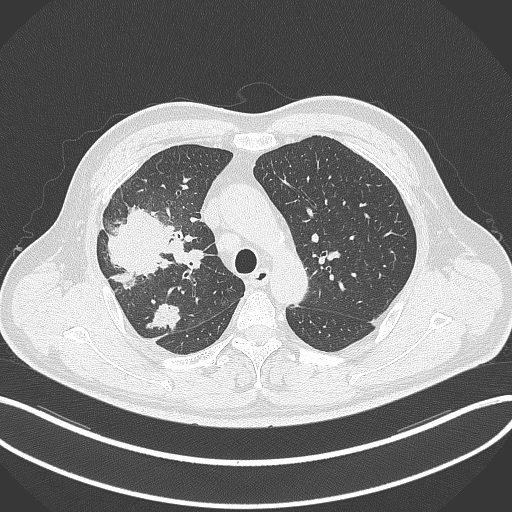
Chest CT, one axial slice. Position 237 of 348 along the scan axis. Lung window (W 1500 / L -600 HU). 1 mm slice thickness. 512 × 512 image matrix. Patient: male, 55 years. Case-level facts recorded for this patient, not image findings: clinical TNM (as recorded): T3 N2 M1.
Annotated regions visible in this slice (bounding box drawn by a radiologist):
- lung tumour (recorded histology: adenocarcinoma): bounding box [x1, y1, x2, y2] px = [99, 202, 176, 288]